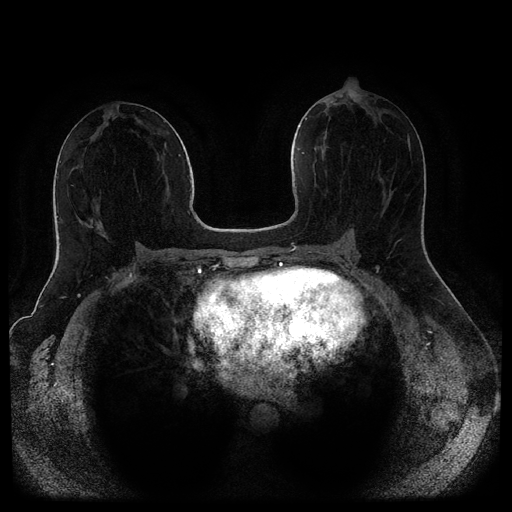
Breast MRI (dynamic contrast-enhanced, multi-phase), one axial slice; dynamic contrast-enhanced series, time point 2 of 5 at this slice position (early post-contrast); 1.5 T; TE 2.6 ms, TR 5.3 ms; 2 mm slice thickness; 512 × 512 image matrix, field of view 370 × 370 mm. Female patient, age 44 years.
Structures marked on this image (semi-automatic segmentation, software-assisted and operator-edited):
- breast lesion (labelled benign in the annotation): box from (x=90, y=220) to (x=107, y=238) px